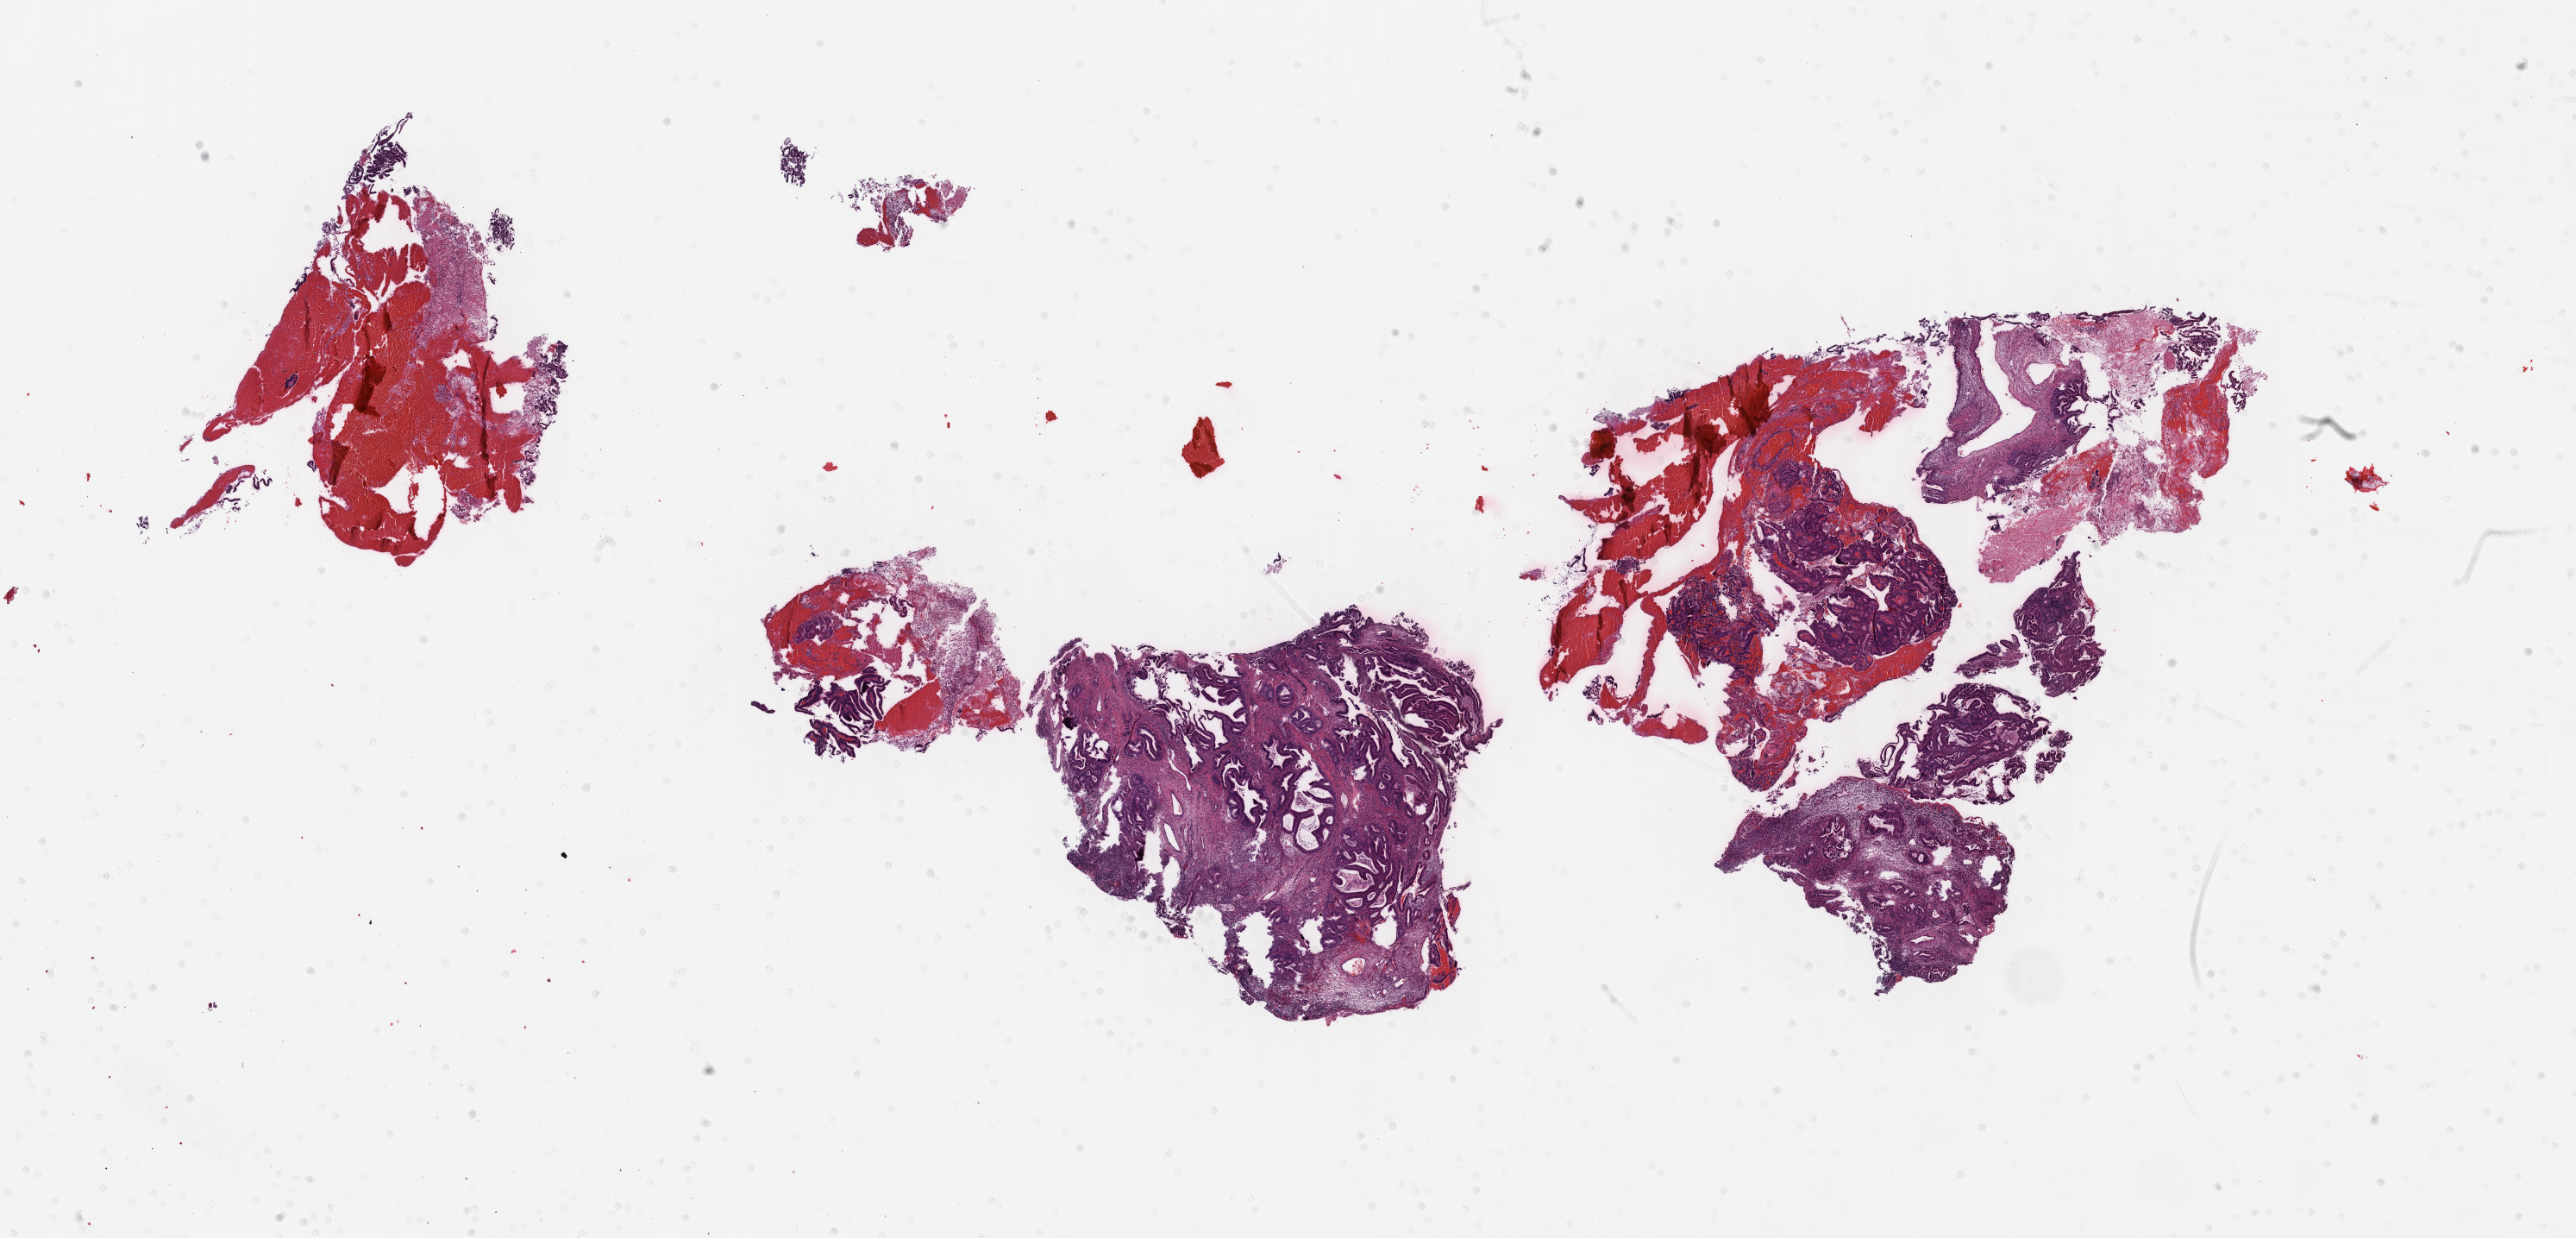
Whole-slide histology image, H&E — shown as a low-resolution overview of the whole scanned area (about 24.2 x 11.6 mm, acquisition: 40x scan). Formalin-fixed paraffin-embedded (FFPE) diagnostic section. Sample: primary tumour, cervix. Patient: female, age at initial diagnosis 44 years. Histologic grade: GX (grade cannot be assessed).
FIGO stage: IB2. Histologic diagnosis: Adenocarcinoma, endocervical type (cervix uteri).